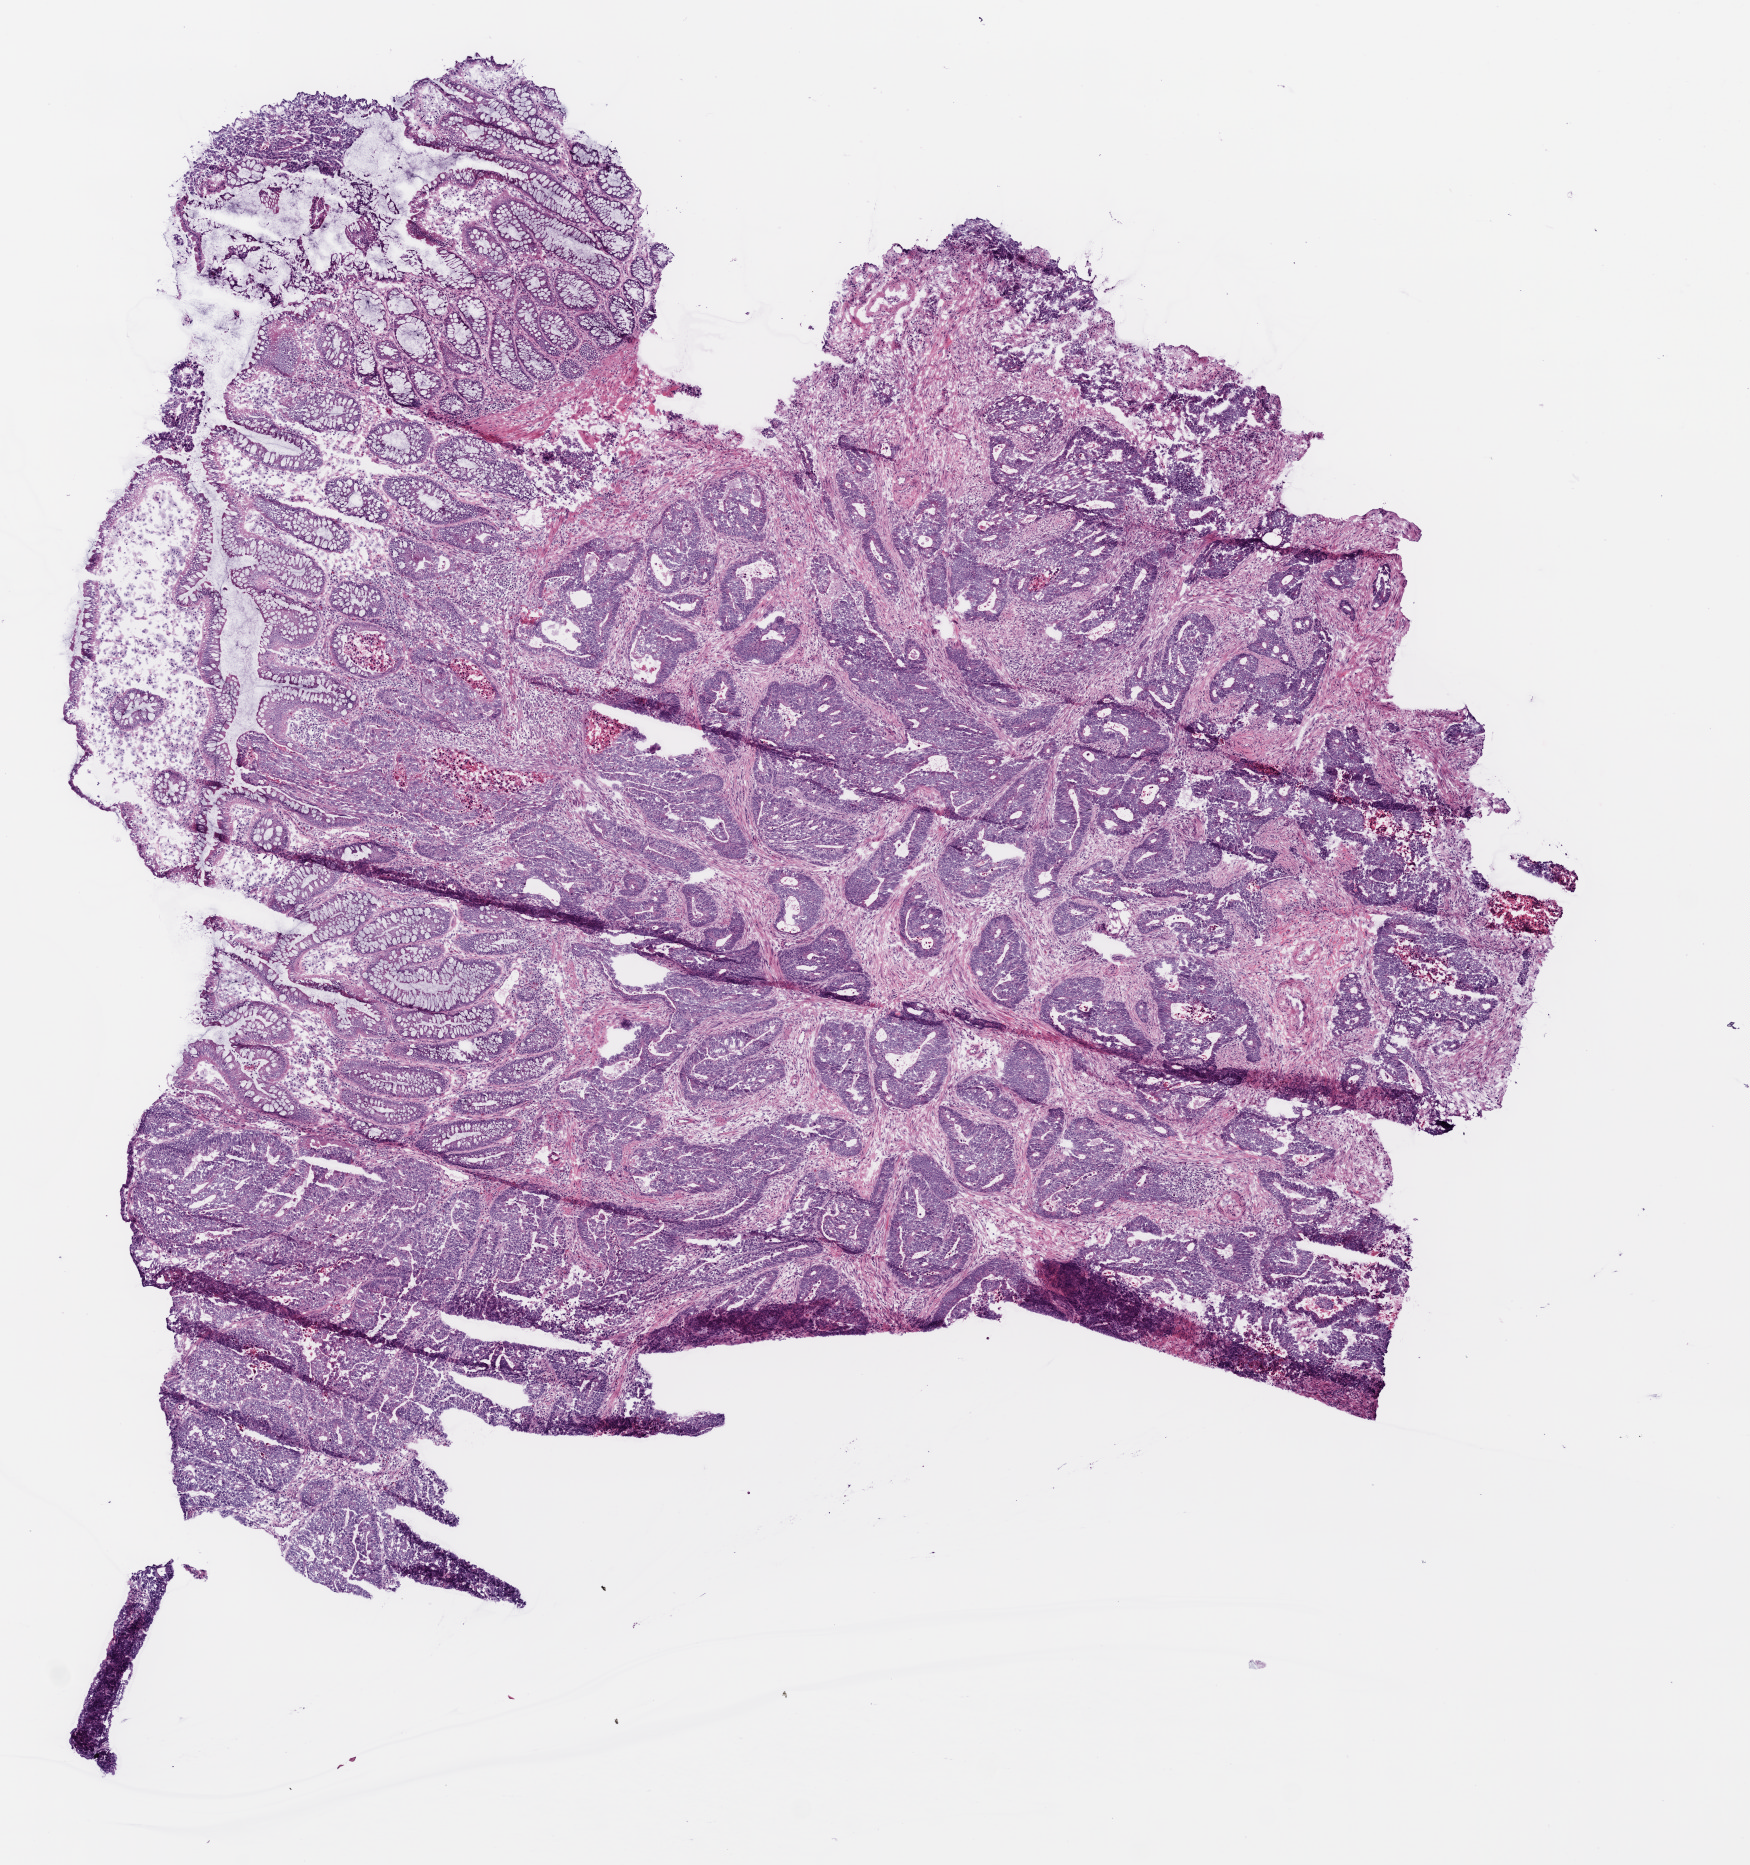
H&E-stained whole-slide image — shown as a low-resolution overview of the whole scanned area (about 7.0 x 7.5 mm, acquisition: 20x scan); frozen section from the bottom of the tissue portion; primary tumour sample from the colon. Male patient; age at initial diagnosis 70 years.
Pathologic diagnosis: Adenocarcinoma, NOS (rectosigmoid junction).